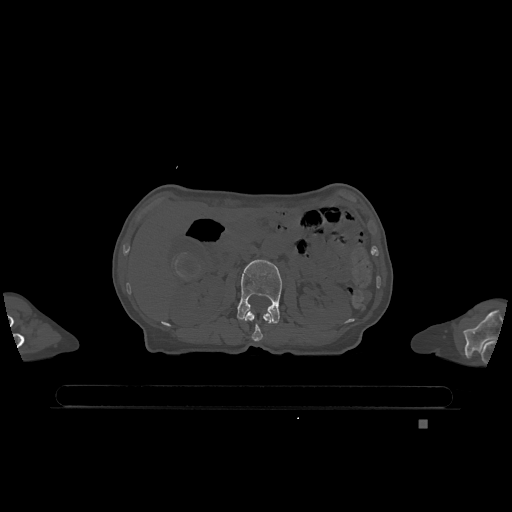
CT including the spine, one axial slice. Position 434 of 1317 along the scan axis. Bone window (W 1800 / L 400 HU). 0.5 mm slice thickness. 512 × 512 image matrix, field of view 500 × 500 mm. Female patient, age 74 years. Case-level facts recorded for this patient, not image findings: primary cancer: lung.
Structures marked on this image (semi-automatically segmented with operator editing):
- L1 vertebra: bounding box <244,310,272,342> (left, top, right, bottom; pixels)
- L2 vertebra: <237,260,282,324>